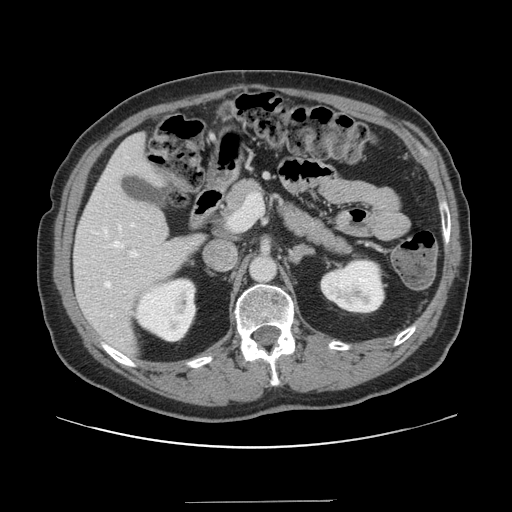
Contrast-enhanced abdominal CT, one axial slice; slice 79 of 151 in the series (ordered by position); 120 kVp; intravenous contrast given; soft-tissue window (W 400 / L 40 HU); 2.5 mm slice thickness; 512 × 512 image matrix, field of view 399 × 399 mm. Male patient, age 63 years. Case-level facts recorded for this patient, not image findings: diagnosis: colorectal cancer liver metastases, imaged before liver resection; multiple liver metastases: no; largest metastasis: 2.1 cm; disease in both lobes: no.
Structures marked on this image (outlined manually by an expert reader):
- hepatic veins: box from (x=104, y=226) to (x=123, y=288) px
- liver: (x=75, y=134)–(x=204, y=354)
- planned liver remnant (the part of the liver to remain after resection): (x=75, y=134)–(x=203, y=355)
- portal vein (with intrahepatic branches): (x=129, y=194)–(x=263, y=258)